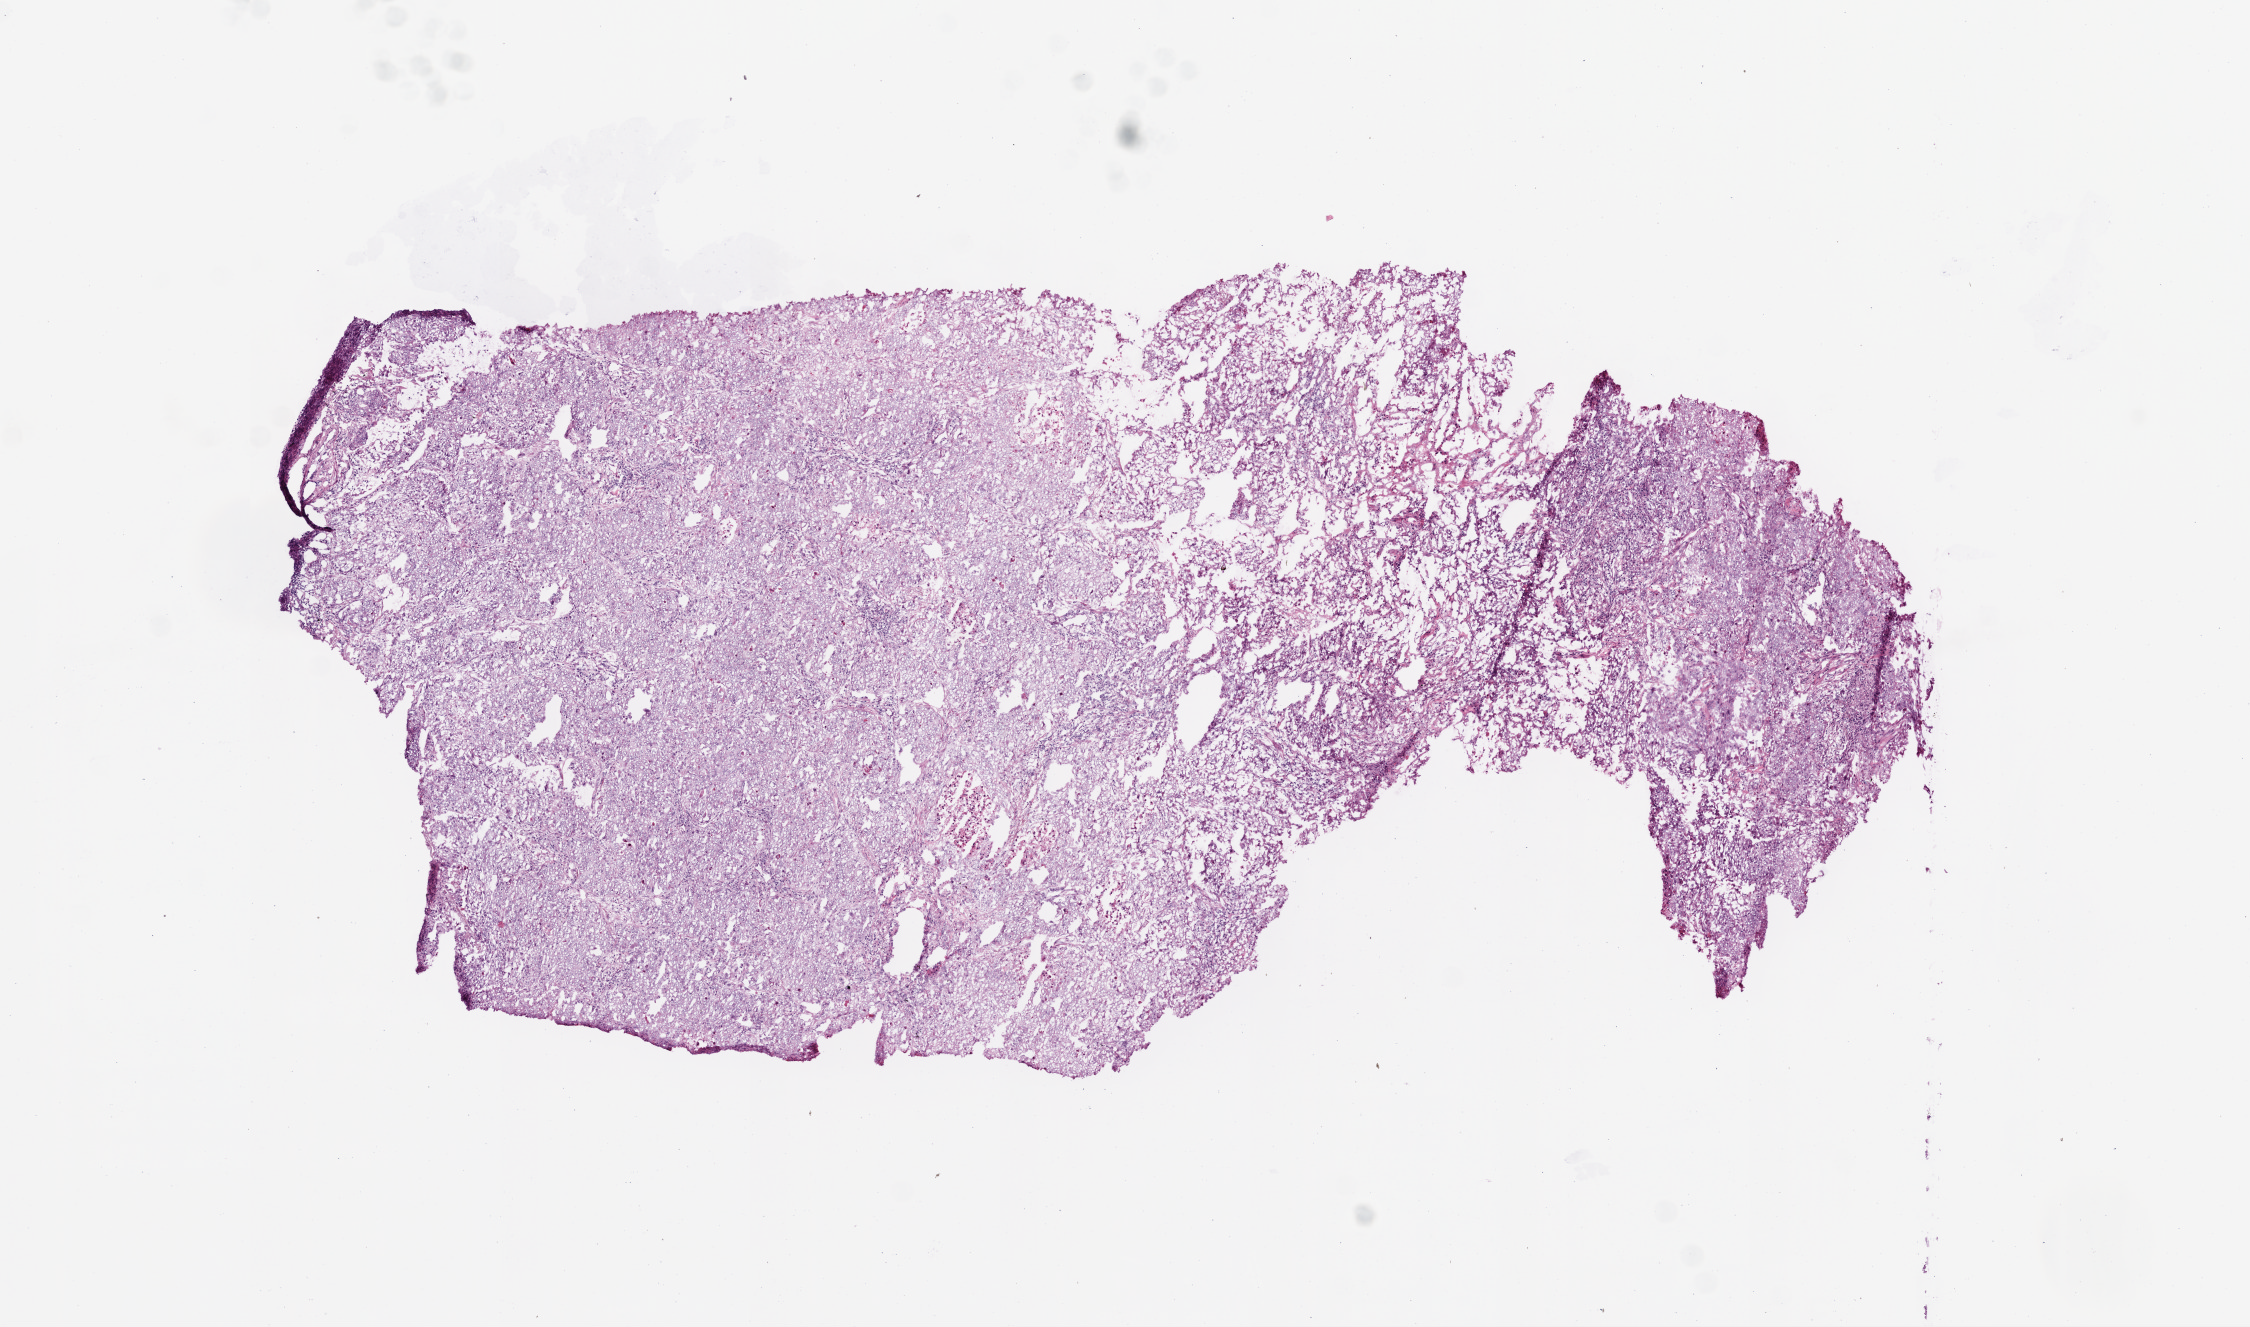
Whole-slide histology image, H&E, low-resolution overview of the scanned area, about 9.0 x 5.3 mm (acquisition: 20x scan); frozen section; sample: primary tumour, lung. Female, age 79 years at initial diagnosis. Pathologist review of this section (percent, as recorded): tumour cells 82%, tumour nuclei 85%, normal cells 10%, stromal cells 5%, necrosis 3%.
* AJCC pathologic stage: IIIA
* histologic diagnosis: Adenocarcinoma, NOS (lower lobe, lung)